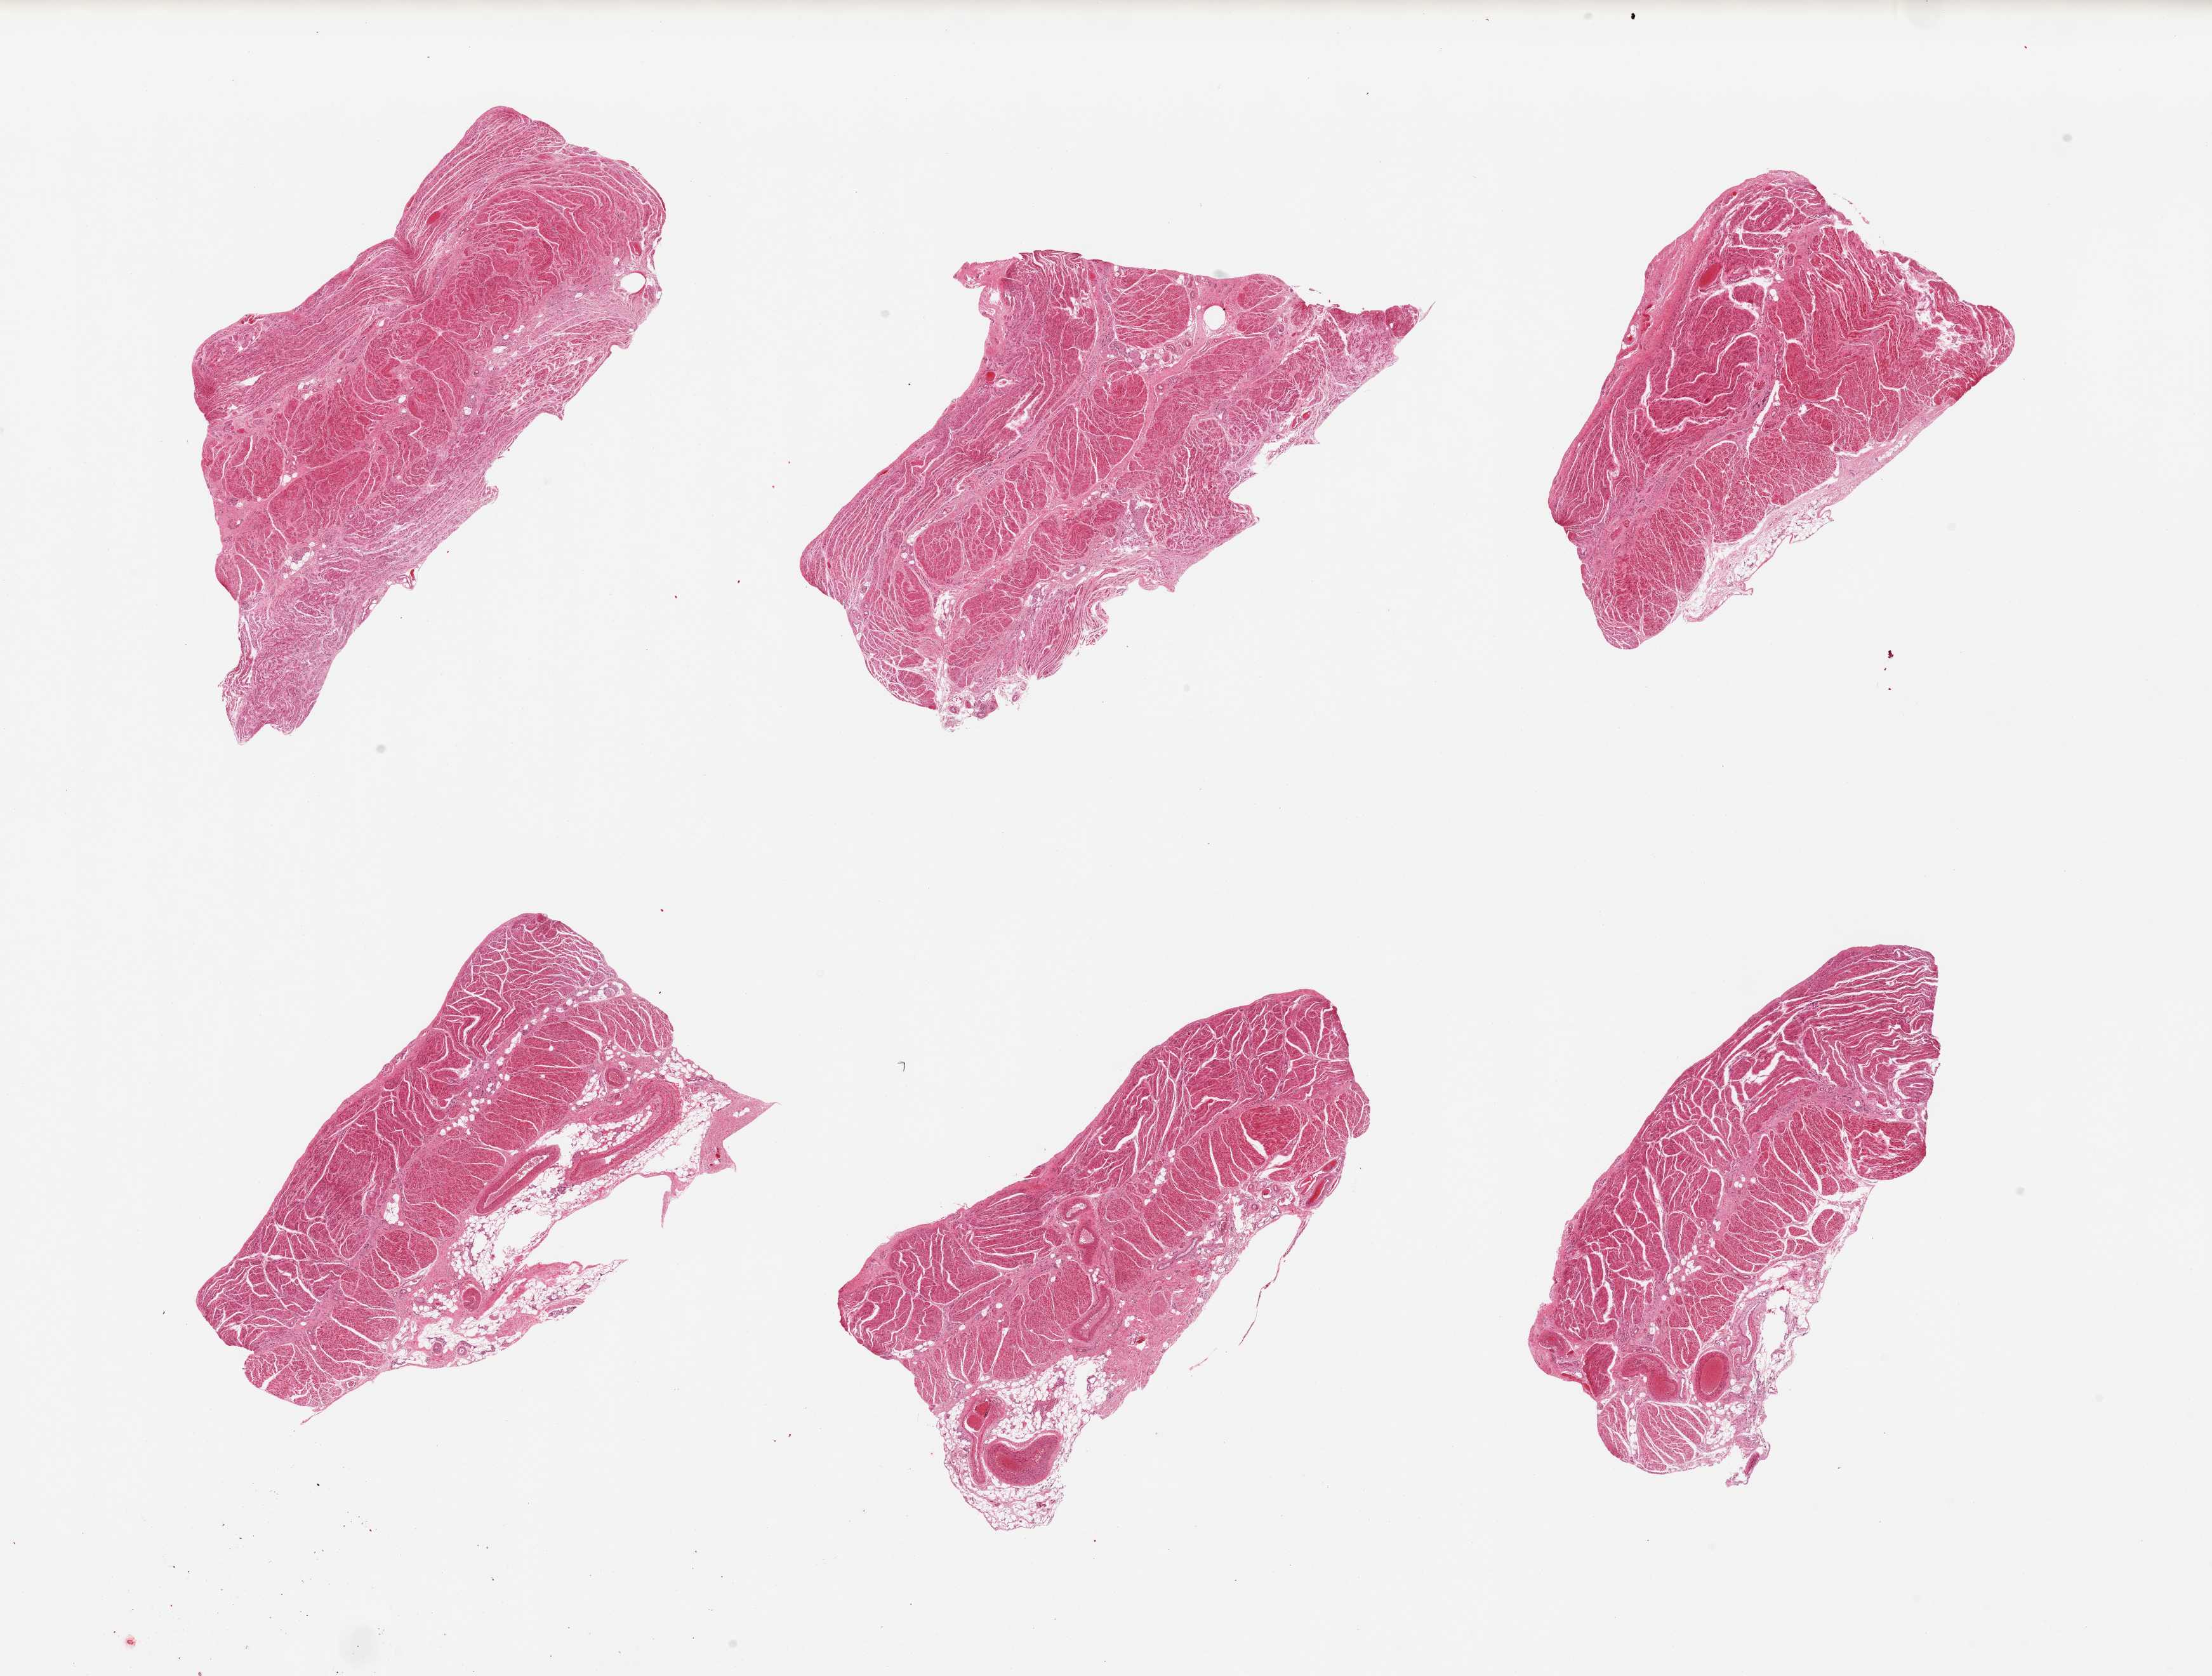
Haematoxylin and eosin whole-slide image, brightfield — shown as a low-resolution overview of the whole scanned area (about 27.6 x 20.9 mm); PAXgene-fixed paraffin-embedded (PFPE) section; sampled site (target tissue): gastroesophageal junction; tissue donor sample. Female donor.
• reviewer comment on this tissue sample: 6 pieces; well trimmed muscle